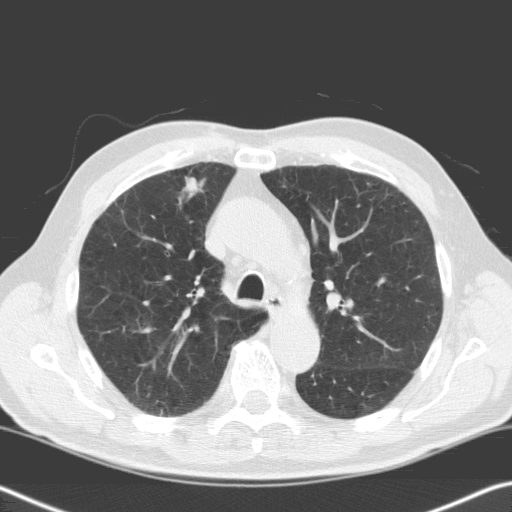
Low-dose screening chest CT, one axial slice; lung window (W 1500 / L -600 HU); 3.2 mm slice thickness; 512 × 512 image matrix.
Annotated regions visible in this slice (outlined manually by an expert reader):
- lesion 1 (tumor, upper lobe of right lung): bounding box (x1, y1, x2, y2) in pixels: (183, 177, 199, 194)